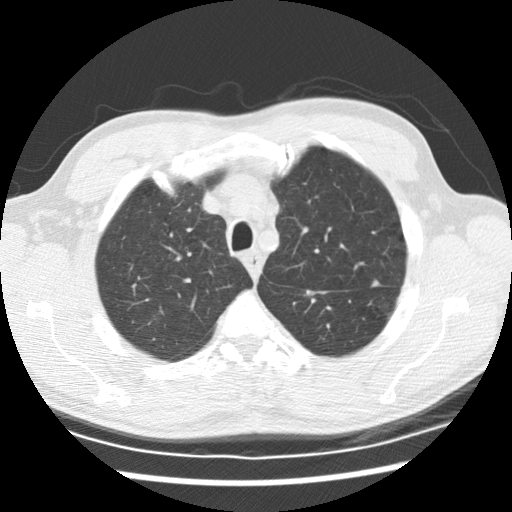
Low-dose screening chest CT, one axial slice; slice 166 of 208 in the series (ordered by position); 120 kVp; lung window (W 1500 / L -600 HU); 512 × 512 image matrix, field of view 340 × 340 mm.
Structures marked on this image (expert manual segmentation):
- lesion 3 (tumor, upper lobe of left lung): bounding box (x1, y1, x2, y2) in pixels: (371, 280, 380, 286)